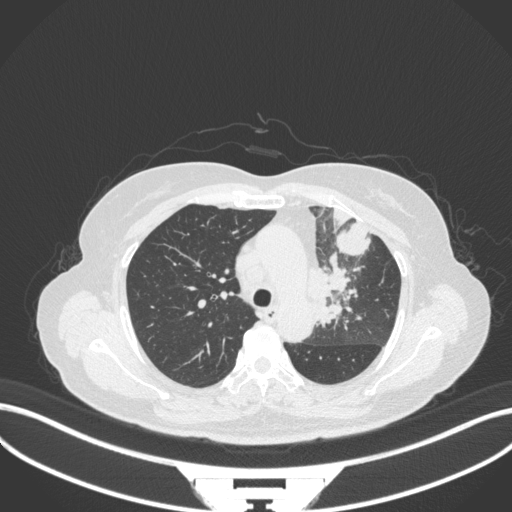
Chest CT, one axial slice; position 237 of 382 along the scan axis; reconstruction kernel B31f; 120 kVp; lung window (W 1500 / L -600 HU); 1 mm slice thickness; 512 × 512 image matrix, field of view 400 × 400 mm. Female patient, age 64 years. Case-level facts recorded for this patient, not image findings: clinical TNM (as recorded): T2a N2 M0.
Structures marked on this image (bounding box drawn by a radiologist):
- lung tumour (recorded histology: adenocarcinoma): bounding box <312,259,364,334> (left, top, right, bottom; pixels)
- lung tumour (recorded histology: adenocarcinoma): <333,216,376,258>